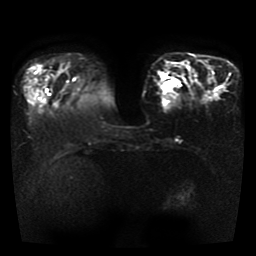
Breast MRI, one axial slice. Position 11 of 41 along the scan axis. Diffusion-weighted series; image 2 of 4 stored at this slice position (different b-values; order by instance number). 1.5 T. 5 mm slice thickness. 256 × 256 image matrix, field of view 330 × 330 mm. Female patient.
Structures marked on this image (expert manual segmentation):
- tumour on diffusion-weighted imaging: box from (x=162, y=80) to (x=177, y=91) px